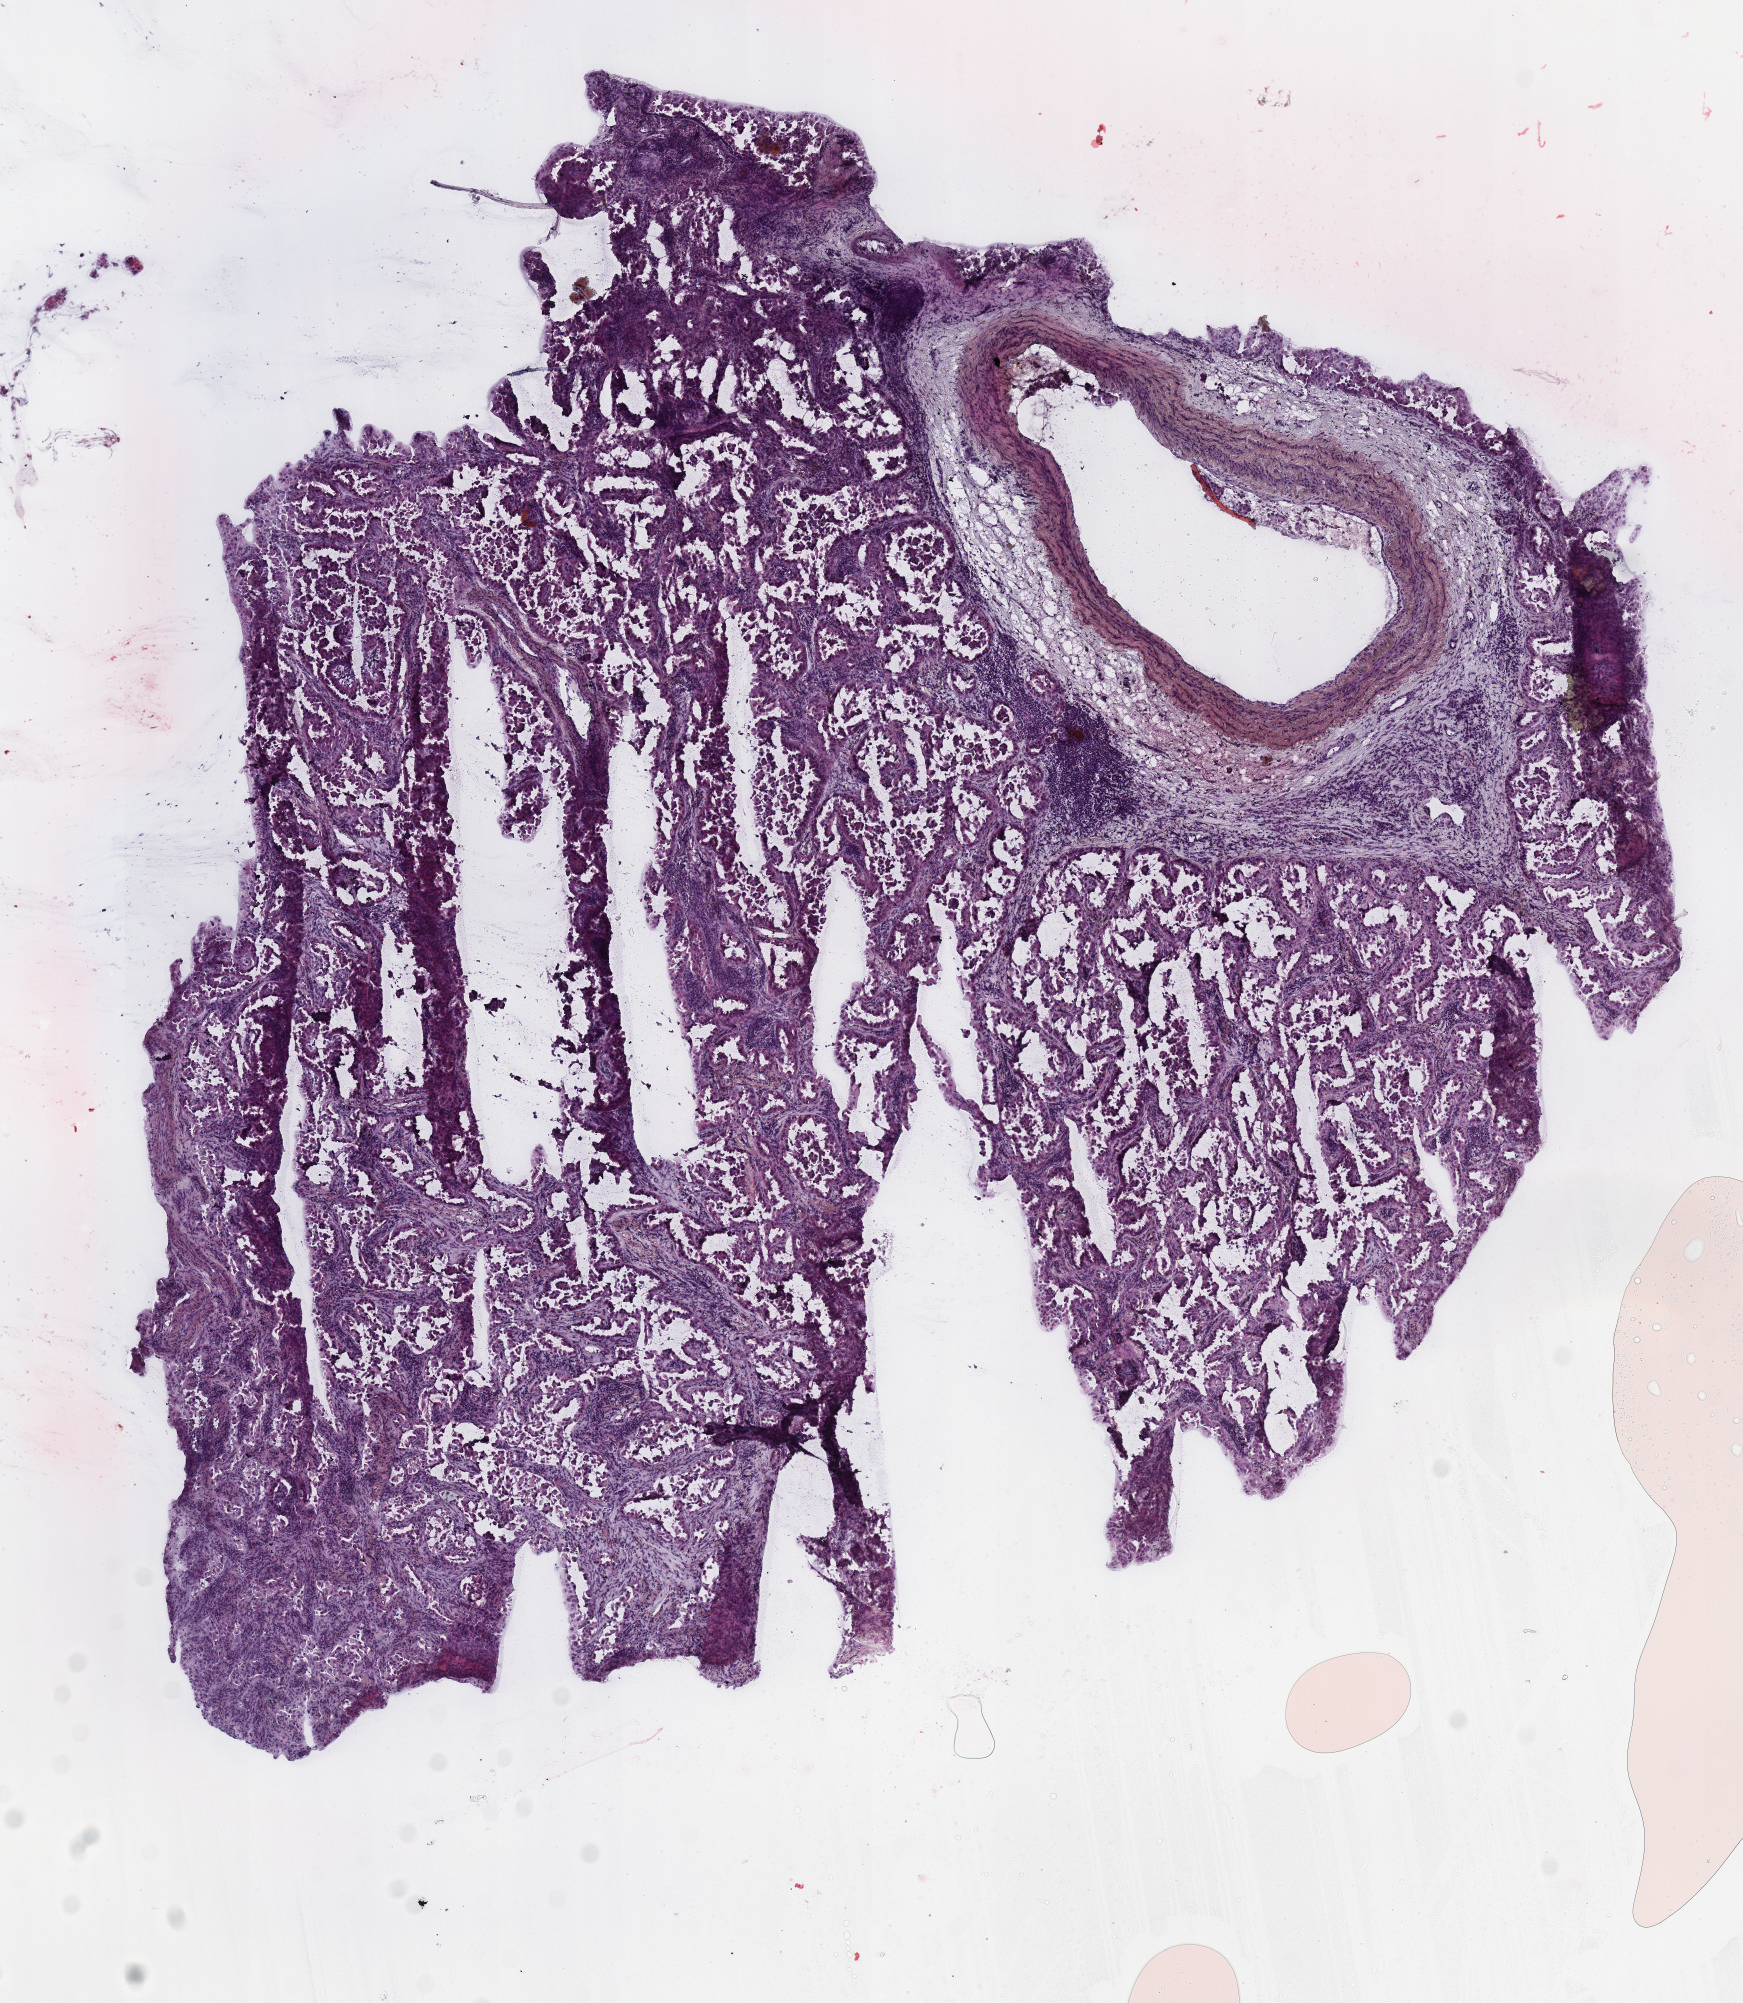
Digitized Hematoxylin and eosin (H&E) stained tissue section (whole slide) — whole scanned area (about 6.9 x 7.9 mm) shown as a low-resolution overview; frozen section; sample: primary tumour, lung. Female, age 70 years at initial diagnosis. Composition of this section per pathologist review: tumour cells 90%, tumour nuclei 65%, normal cells 10%, stromal cells 0%, necrosis 0%. Infiltration values recorded for this section: lymphocyte infiltration 20%, monocyte infiltration 5%.
Pathologic diagnosis: Adenocarcinoma with mixed subtypes (lower lobe, lung). TNM: T3 N0 M0. AJCC pathologic stage: IIB.